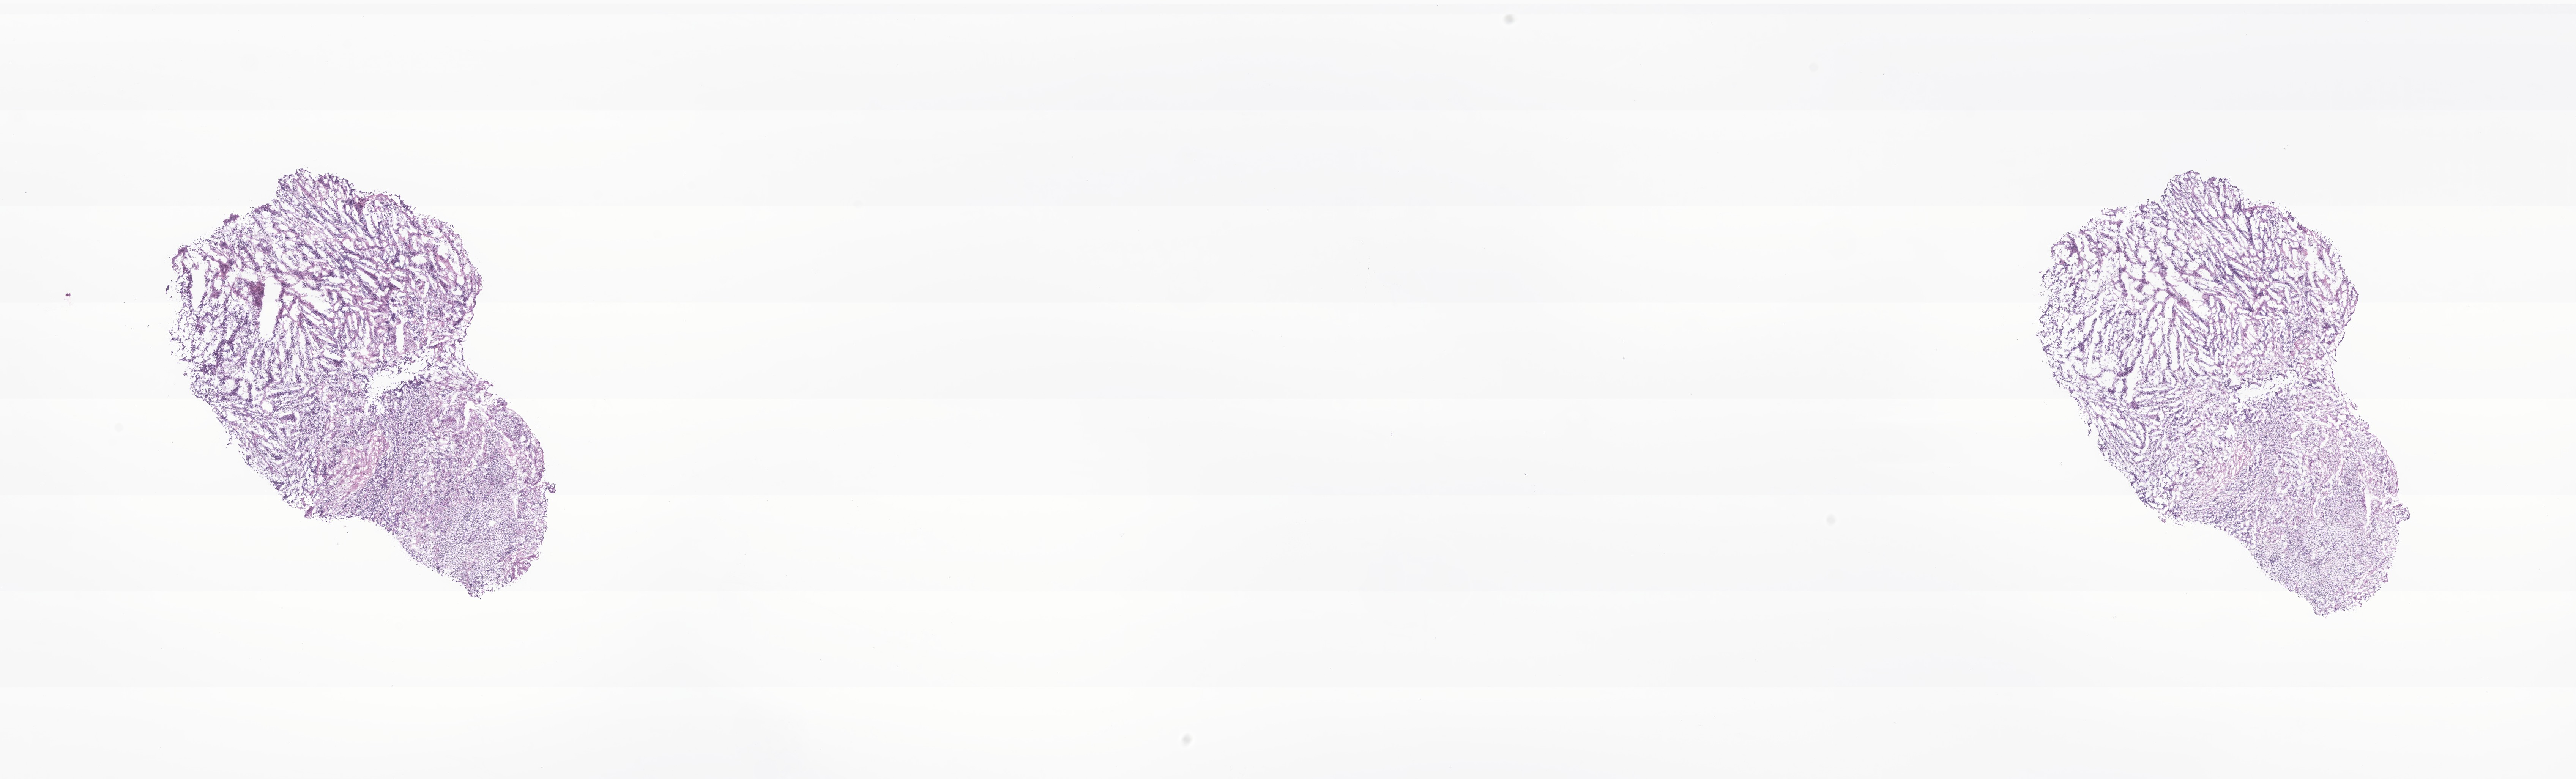
Haematoxylin and eosin whole-slide image of tumor tissue from the anterior mediastinum — shown as a low-resolution overview of the whole scanned area (about 28.6 x 8.7 mm). Cryosection (OCT / tissue freezing medium). Male patient, age 73 months (6 years 1 month).
Recorded diagnosis: Neuroblastoma, NOS.